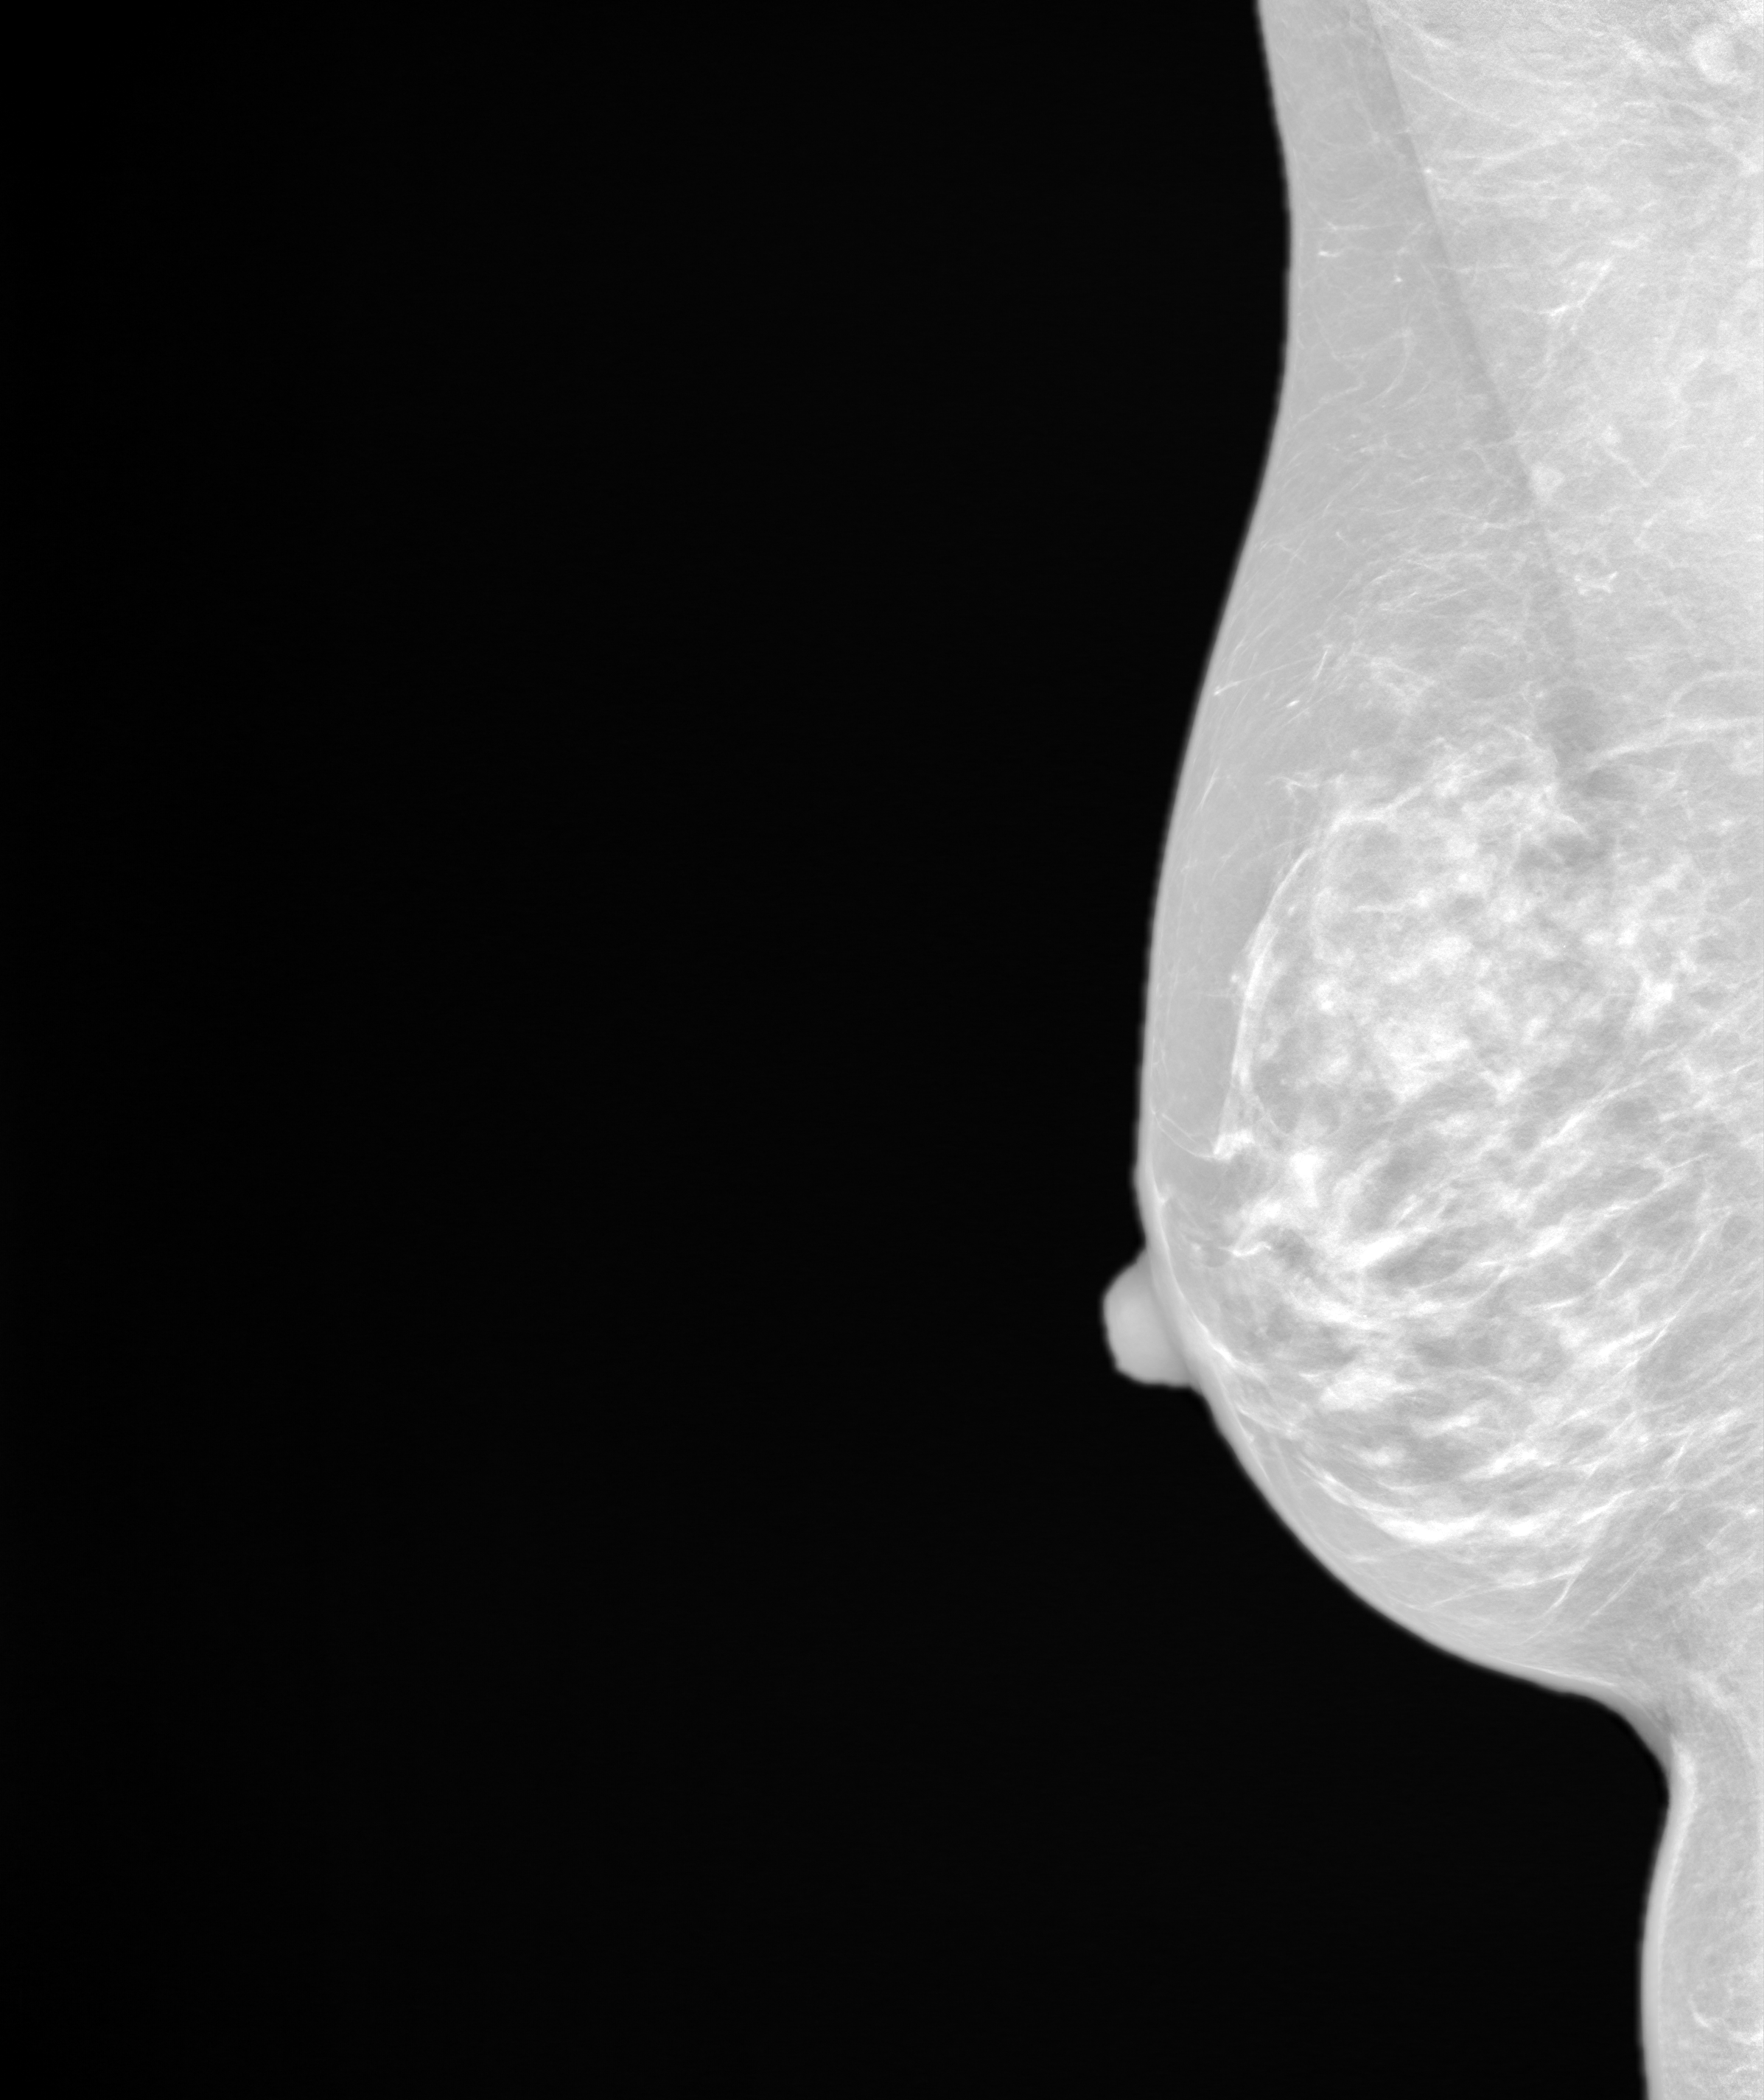
Screening examination. Patient aged 59 years (female).
Image type: synthesized 2-D view from tomosynthesis. Breast: right. Projection: mediolateral oblique (MLO) view.